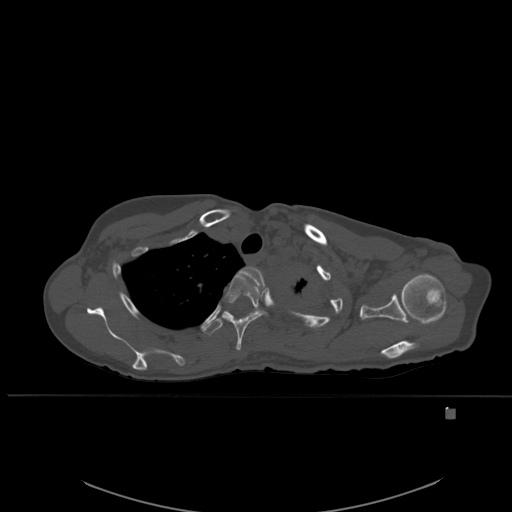
CT including the spine, one axial slice; slice 423 of 537 in the series (ordered by position); bone window (W 1800 / L 400 HU); 1.5 mm slice thickness; 512 × 512 image matrix, field of view 440 × 440 mm. Female patient, age 45 years. Case-level facts recorded for this patient, not image findings: primary cancer: lung.
Annotated regions visible in this slice (semi-automatic segmentation, software-assisted and operator-edited):
- T2 vertebra: bounding box (x1, y1, x2, y2) in pixels: (238, 266, 266, 293)
- T3 vertebra: (224, 273, 266, 351)
- T4 vertebra: (202, 310, 230, 335)